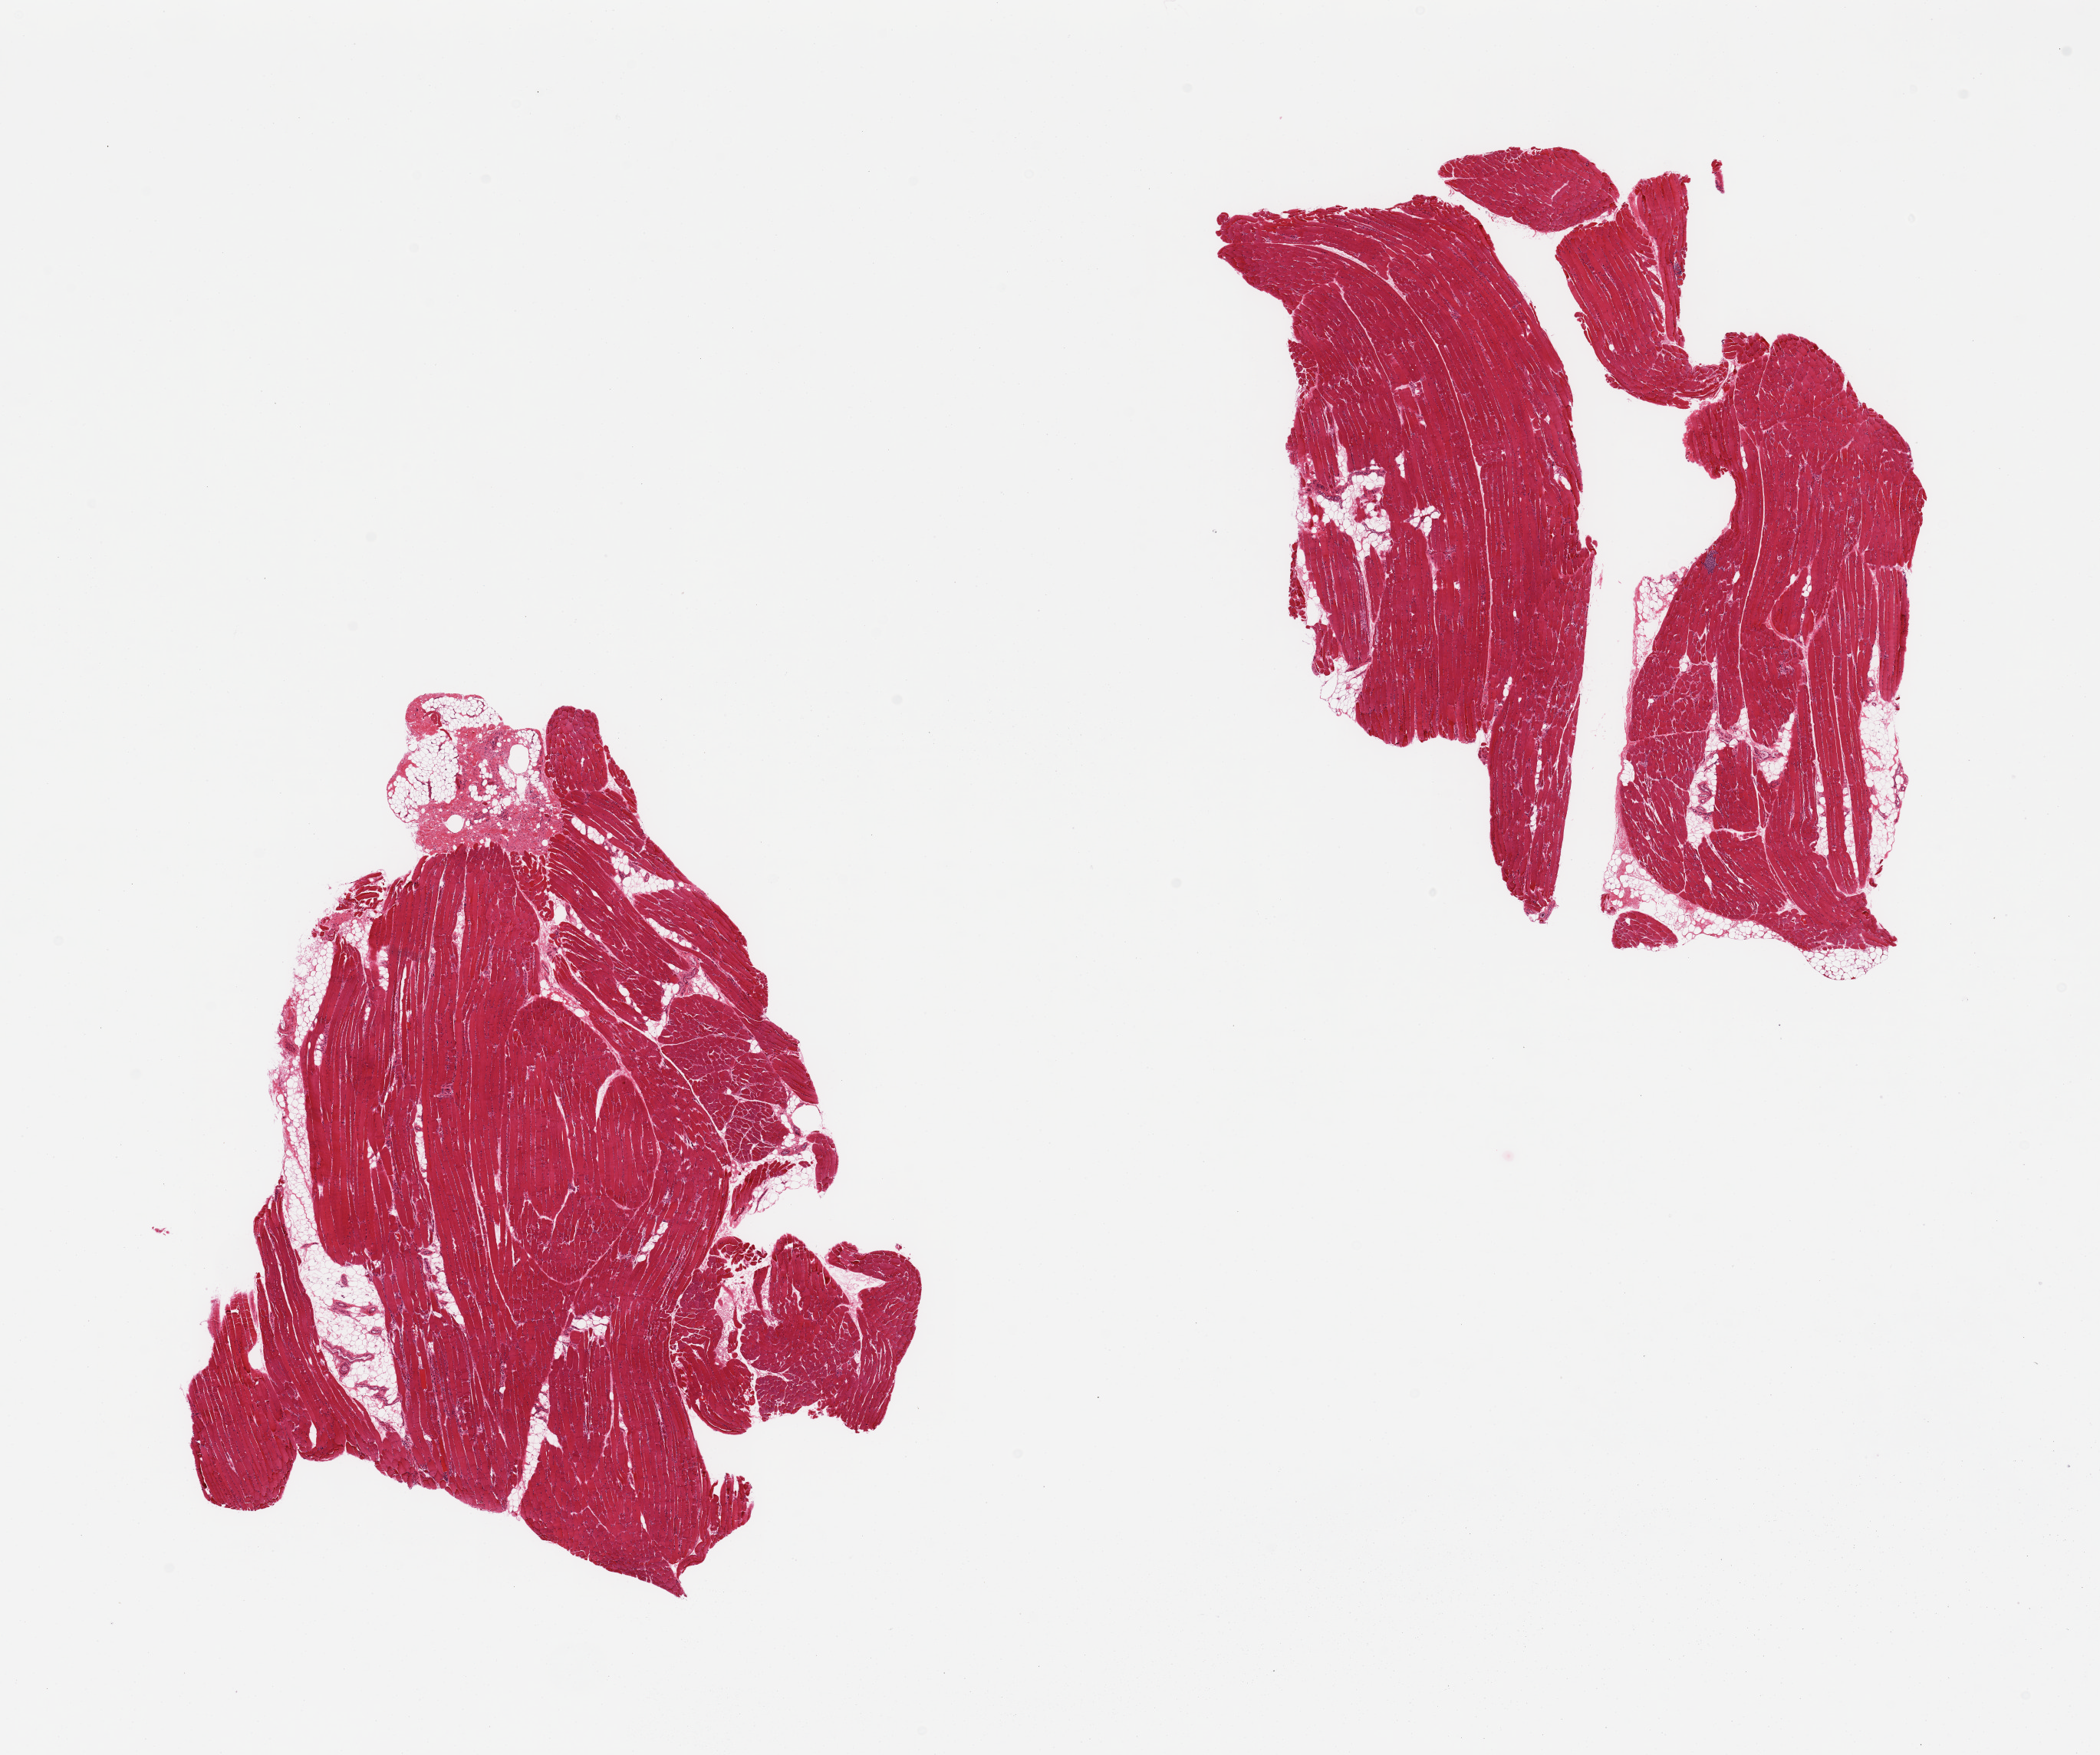
Digitized haematoxylin and eosin-stained section, a low-resolution overview of the entire scanned area, about 21.7 x 18.1 mm; PAXgene-fixed, paraffin-embedded tissue; target tissue: skeletal muscle; tissue donor sample. Donor: female.
Reviewer comment on this tissue sample: 2 pieces, ~10% interstitial fibroadipose/vascular tissue.